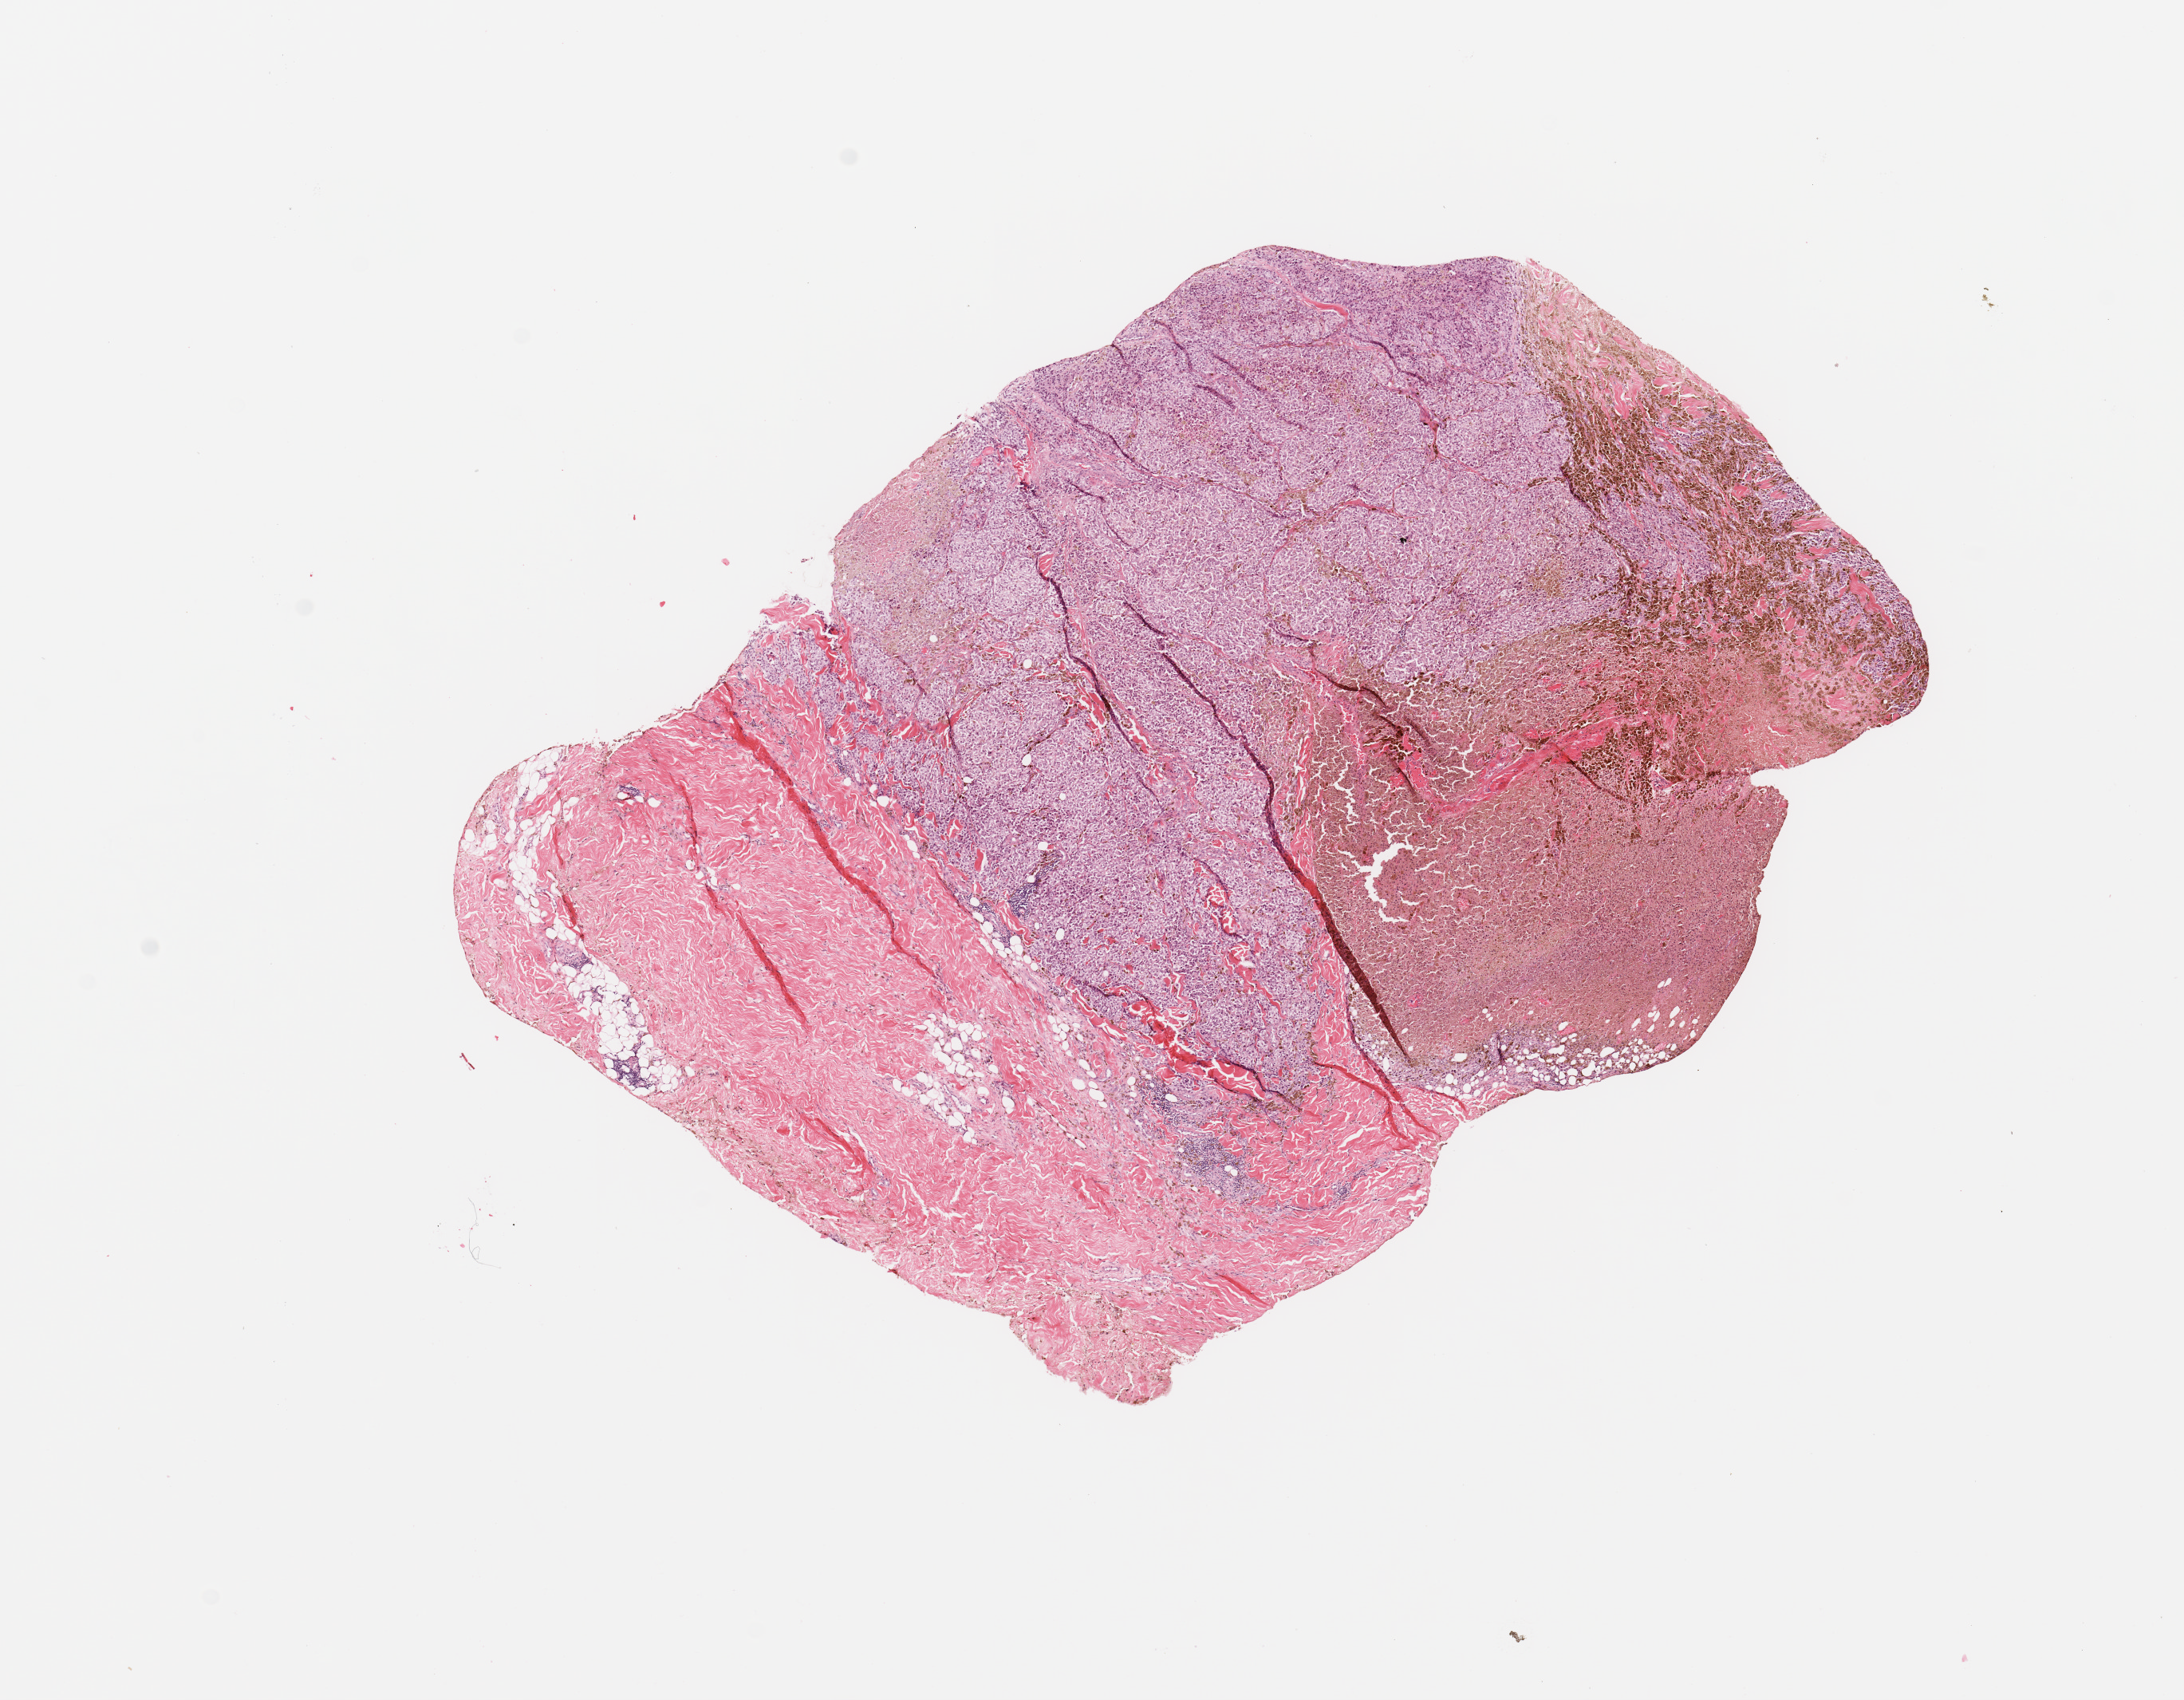
Digitized Hematoxylin and eosin (H&E) stained tissue section (whole slide) — a low-resolution overview of the entire scanned area, about 10.8 x 8.4 mm. Melanoma tumour tissue; sampled site not recorded. Patient: female, age 81 years.
* diagnosis: Malignant melanoma, NOS
* AJCC pathologic stage: IIC
* primary tumour site (as recorded): trunk